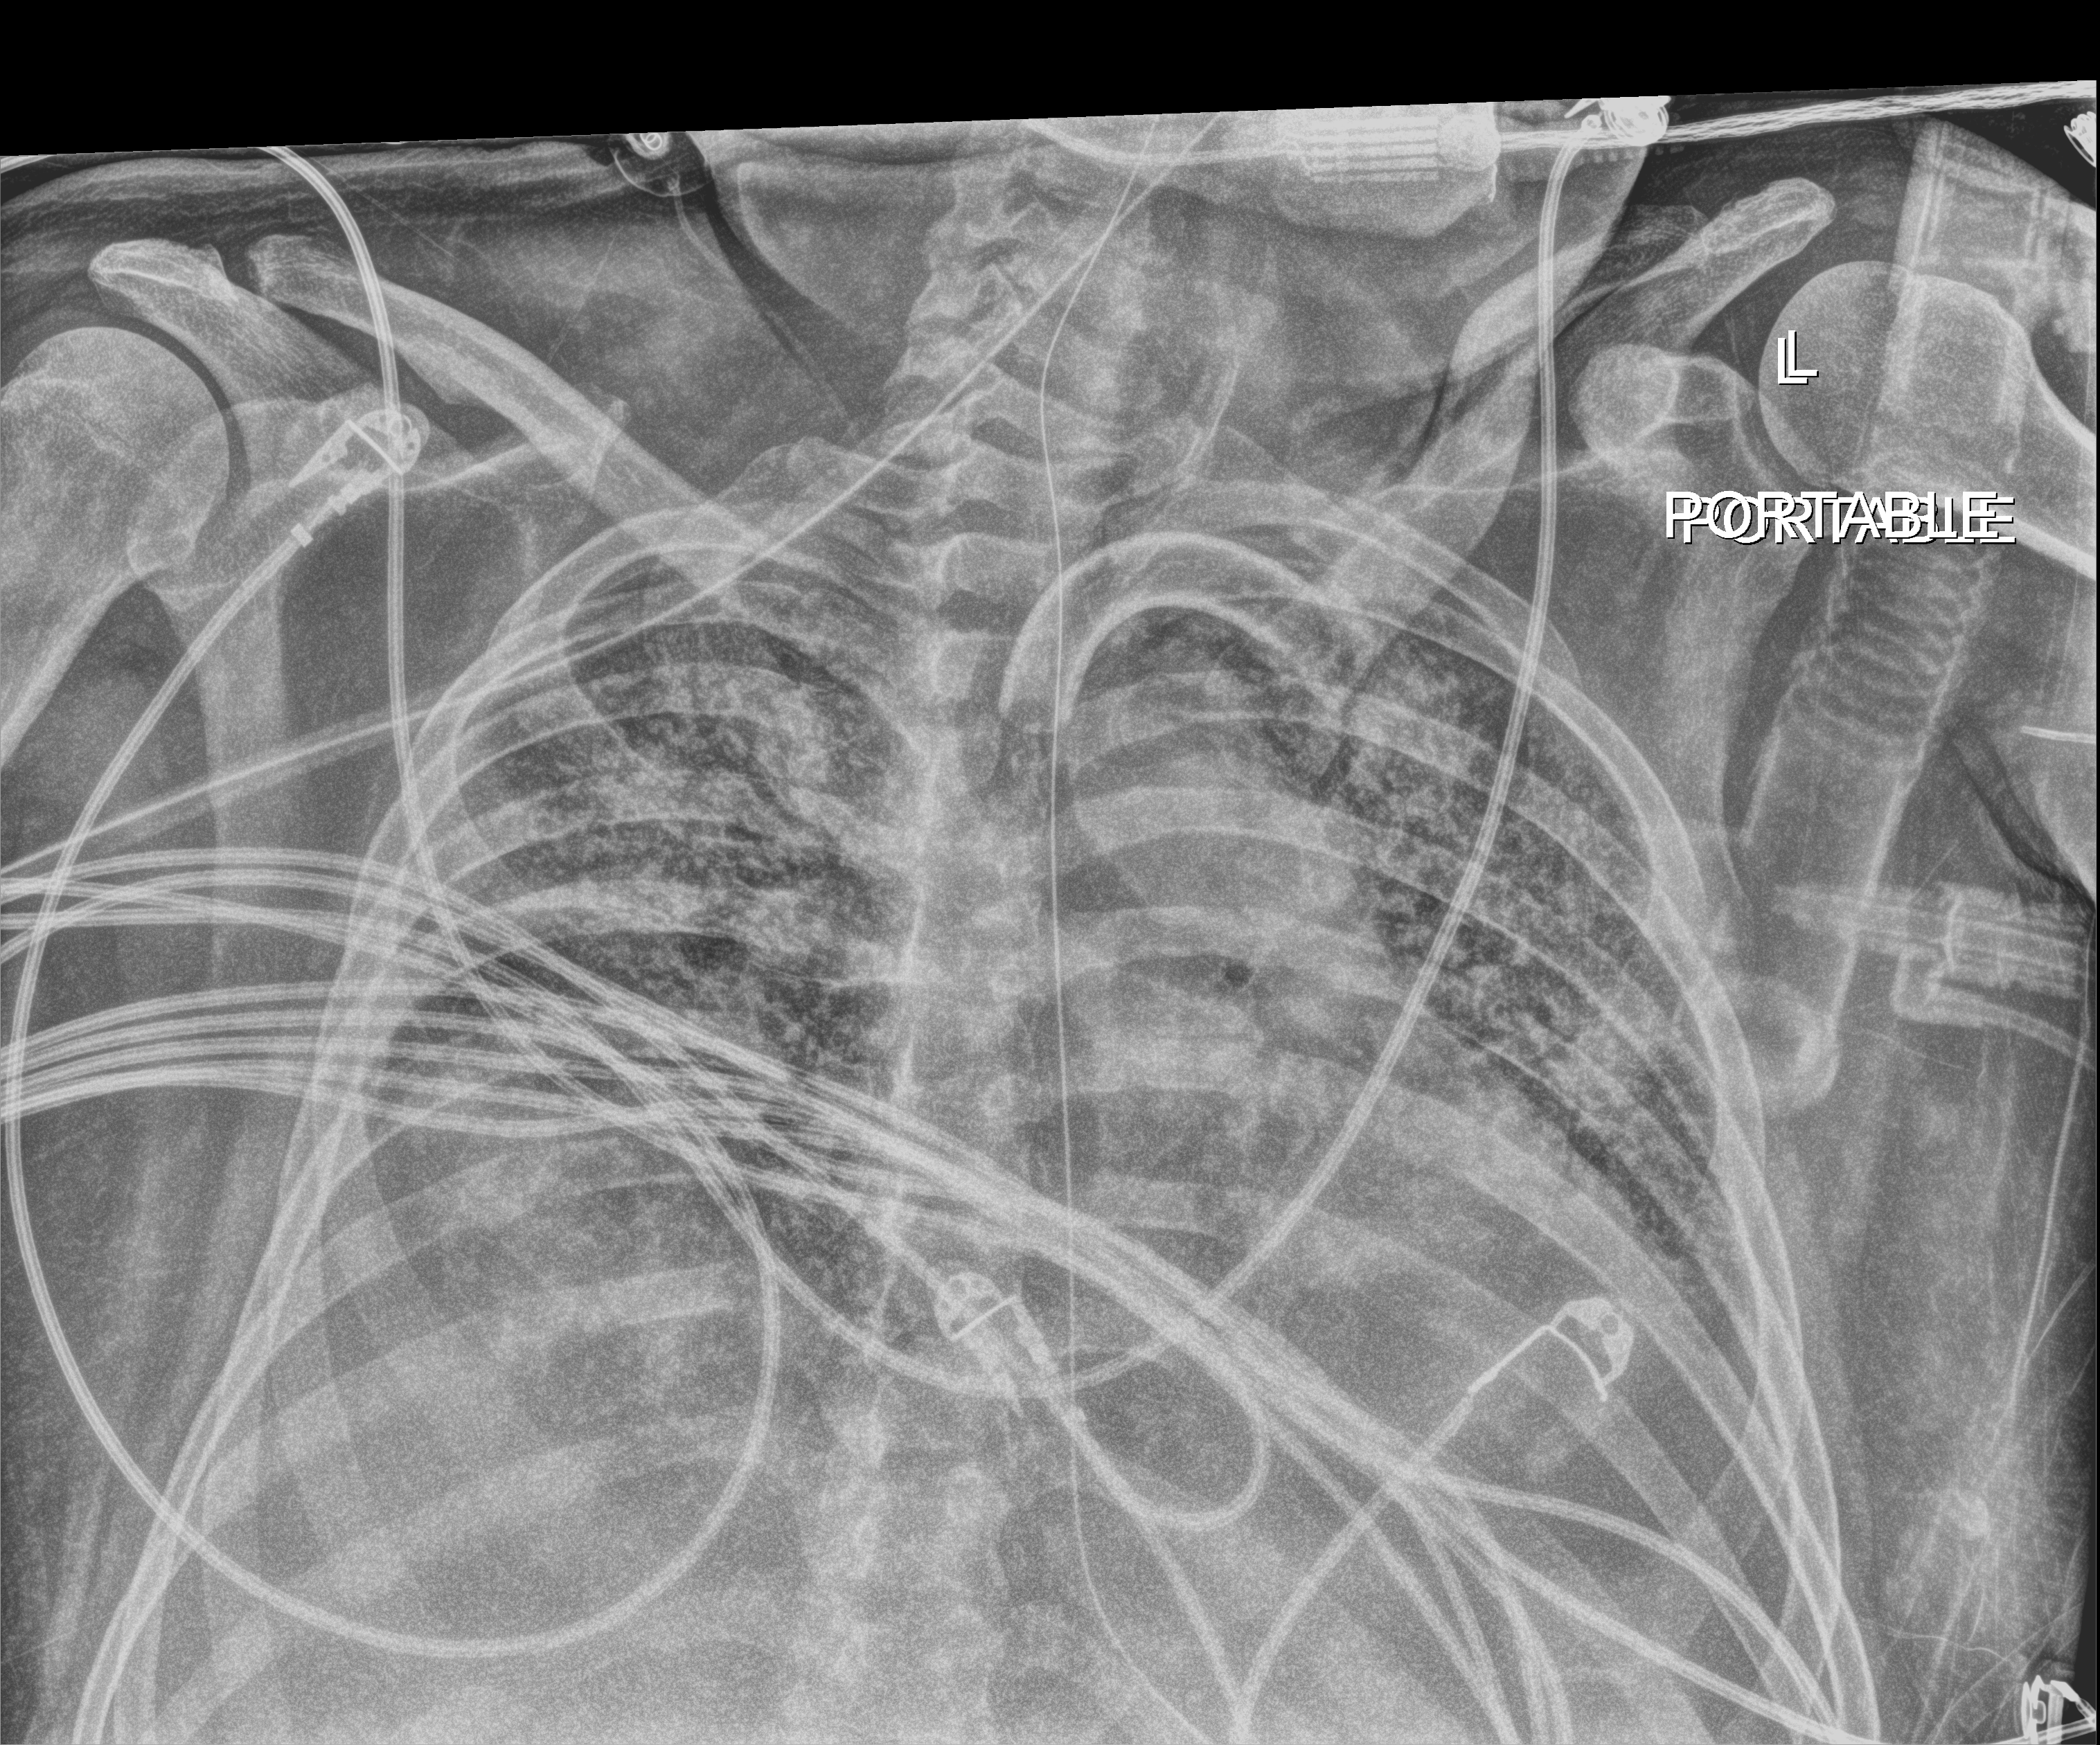
Portable chest radiograph; anteroposterior (AP) projection. Patient hospitalised with COVID-19; male, aged 18–59 years.
From the hospital-stay record, not from the radiograph (when in the stay this image was taken is not recorded):
- length of hospital stay: 96 days
- mechanically ventilated during this hospital stay: yes
- diabetes (admission record): no